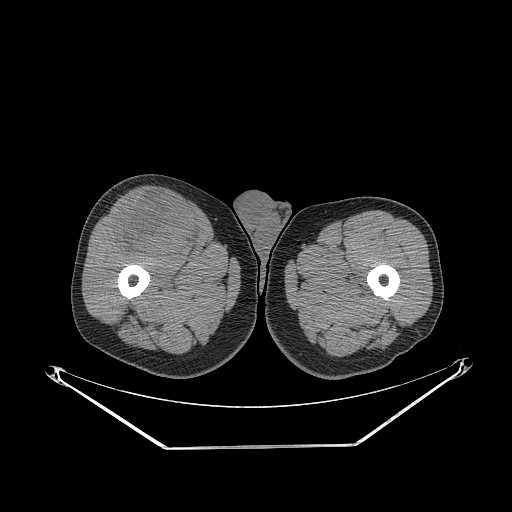
CT of an extremity soft-tissue mass (from a PET/CT study), one axial slice; position 279 of 311 along the scan axis; reconstruction kernel STANDARD; 140 kVp; soft-tissue window (W 400 / L 40 HU); 3.75 mm slice thickness; 512 × 512 image matrix. Male patient. From the clinical record (not read from this slice): histological type: pleiomorphic leiomyosarcoma; grade: intermediate; site of the primary tumour: right thigh.
Structures marked on this image (expert contour drawn on MRI and transferred to this co-registered scan by the dataset authors):
- gross tumour volume including surrounding oedema: bounding box <112,192,200,259> (left, top, right, bottom; pixels)
- gross tumour volume (mass): <112,192,200,259>